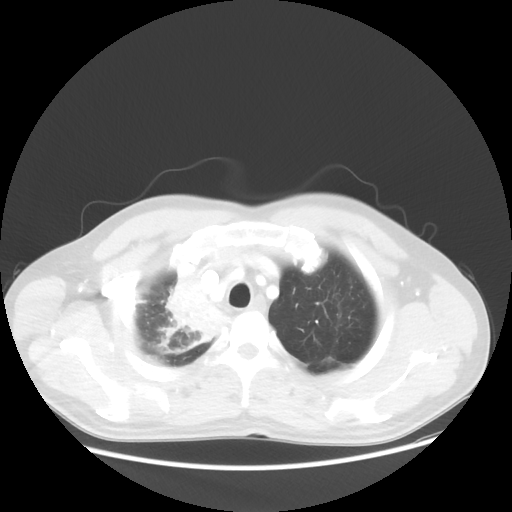
Chest CT, one axial slice; position 46 of 56 along the scan axis; reconstruction kernel STANDARD; lung window (W 1500 / L -600 HU); 5 mm slice thickness; 512 × 512 image matrix, field of view 398 × 398 mm. Male patient, age 60 years. From the clinical record (not read from this slice): clinical TNM (as recorded): T2a N1 M0.
Outlined on this slice (rectangle marked by the reading radiologist):
- lung tumour (recorded histology: squamous cell carcinoma): box from (x=148, y=261) to (x=232, y=352) px